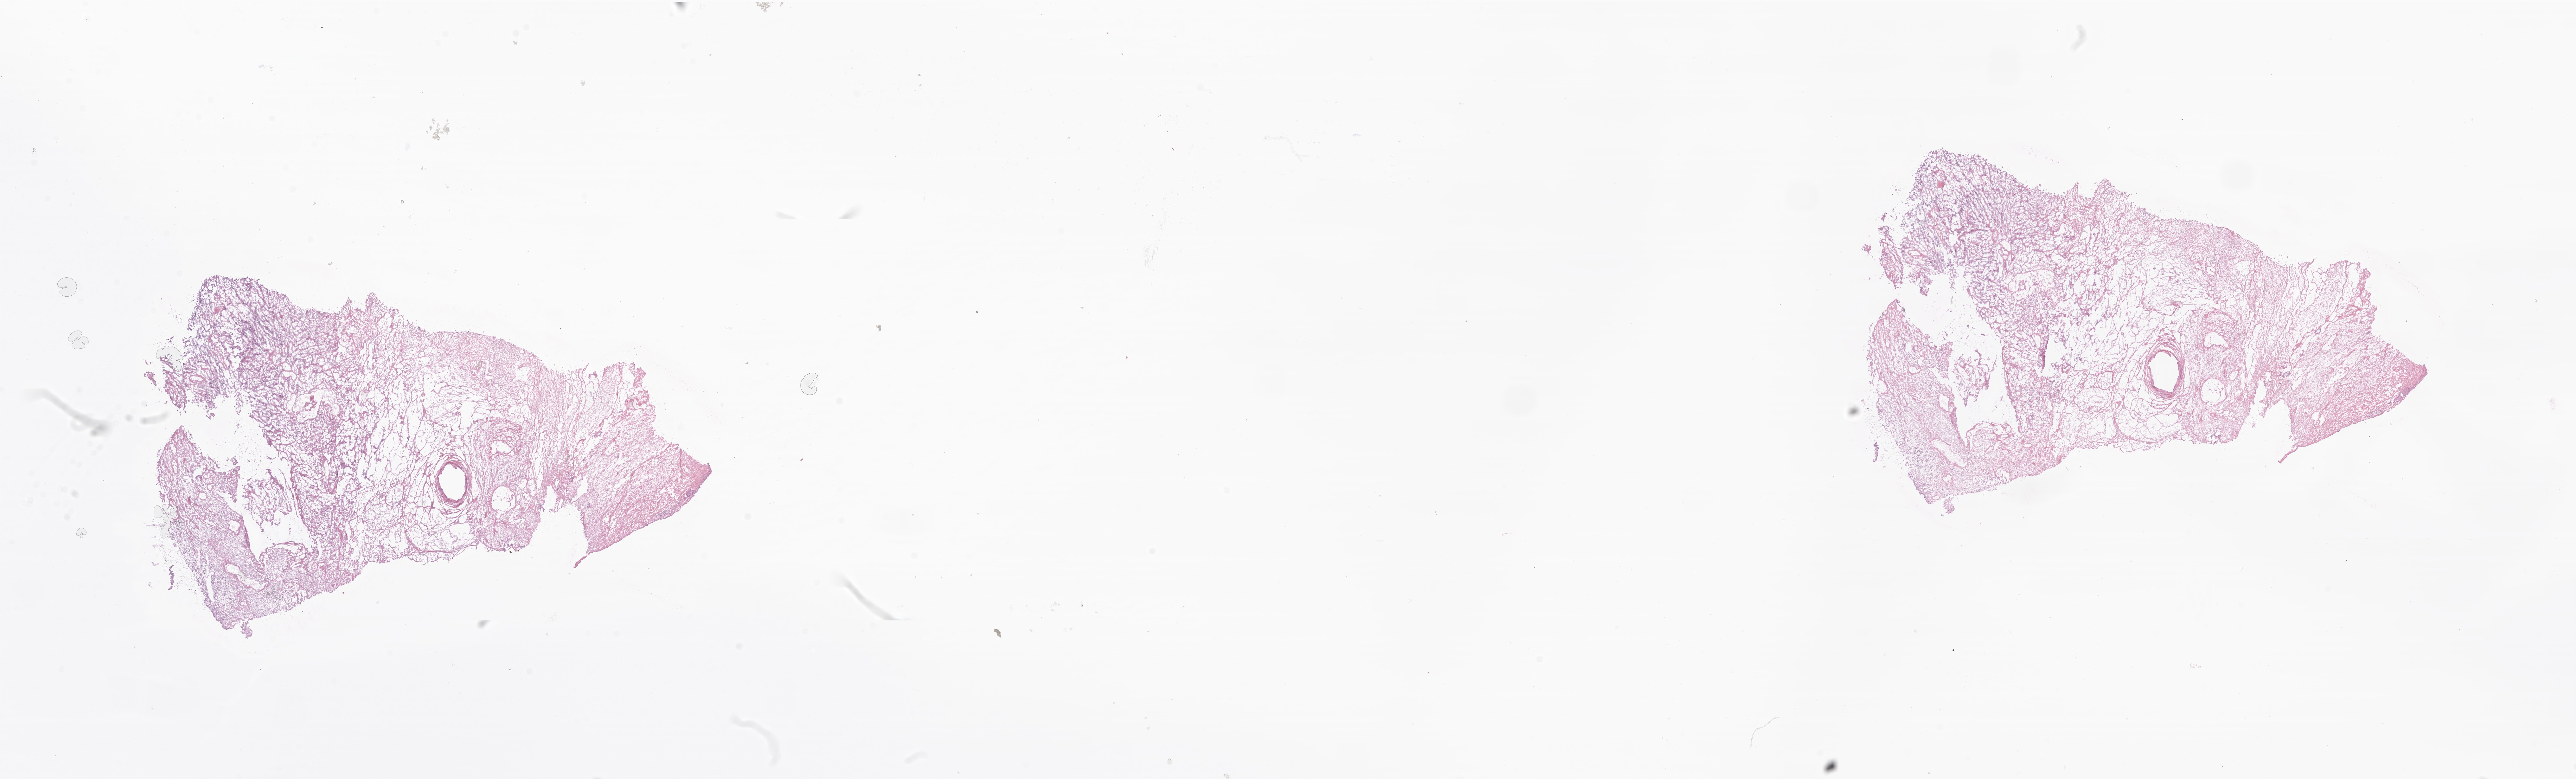
Digitized hematoxylin and eosin (H&E)-stained section of tumor tissue from the nasal cavity — low-resolution overview of the scanned area, about 34.3 x 10.4 mm; frozen section. Patient male; age 93 months (7 years 9 months).
* diagnosis: Neoplasm, malignant